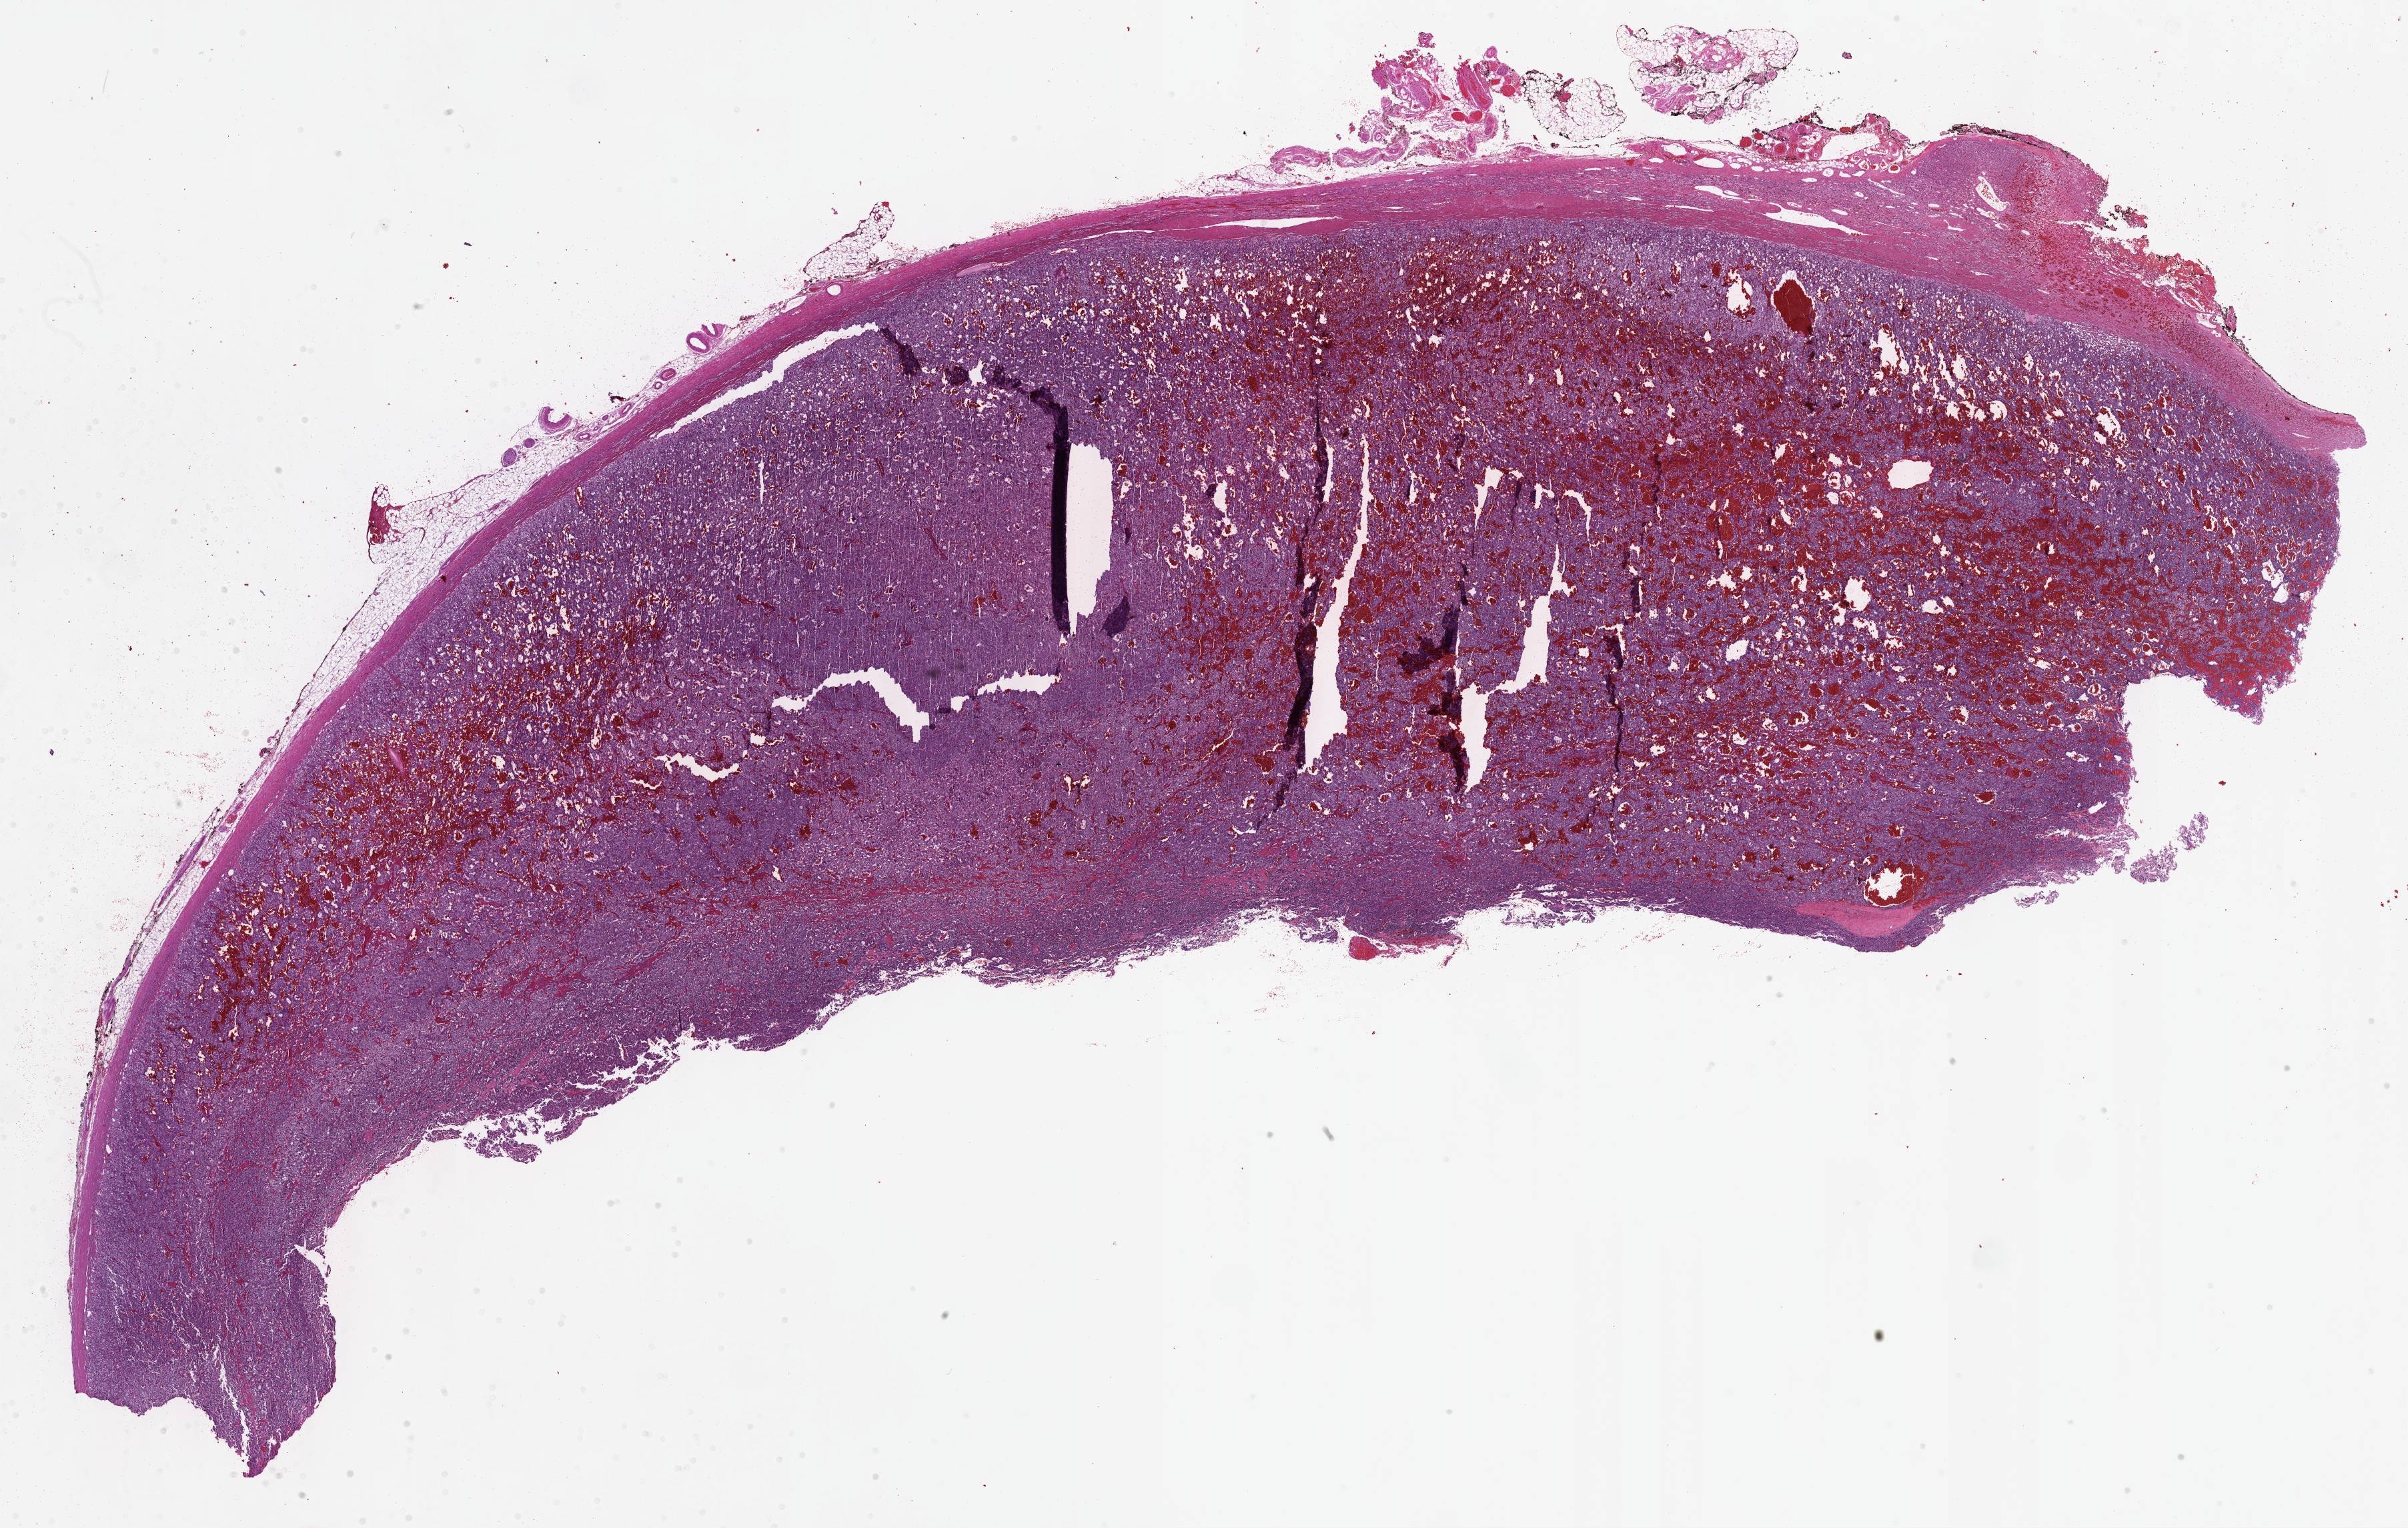
Hematoxylin and eosin (H&E) stained whole-slide image — whole scanned area (about 29.2 x 18.5 mm, acquisition: 40x scan) shown as a low-resolution overview. FFPE section. Adrenal gland, primary tumour sample. Female patient; age at initial diagnosis 56 years.
Pathologic diagnosis: Pheochromocytoma, NOS.